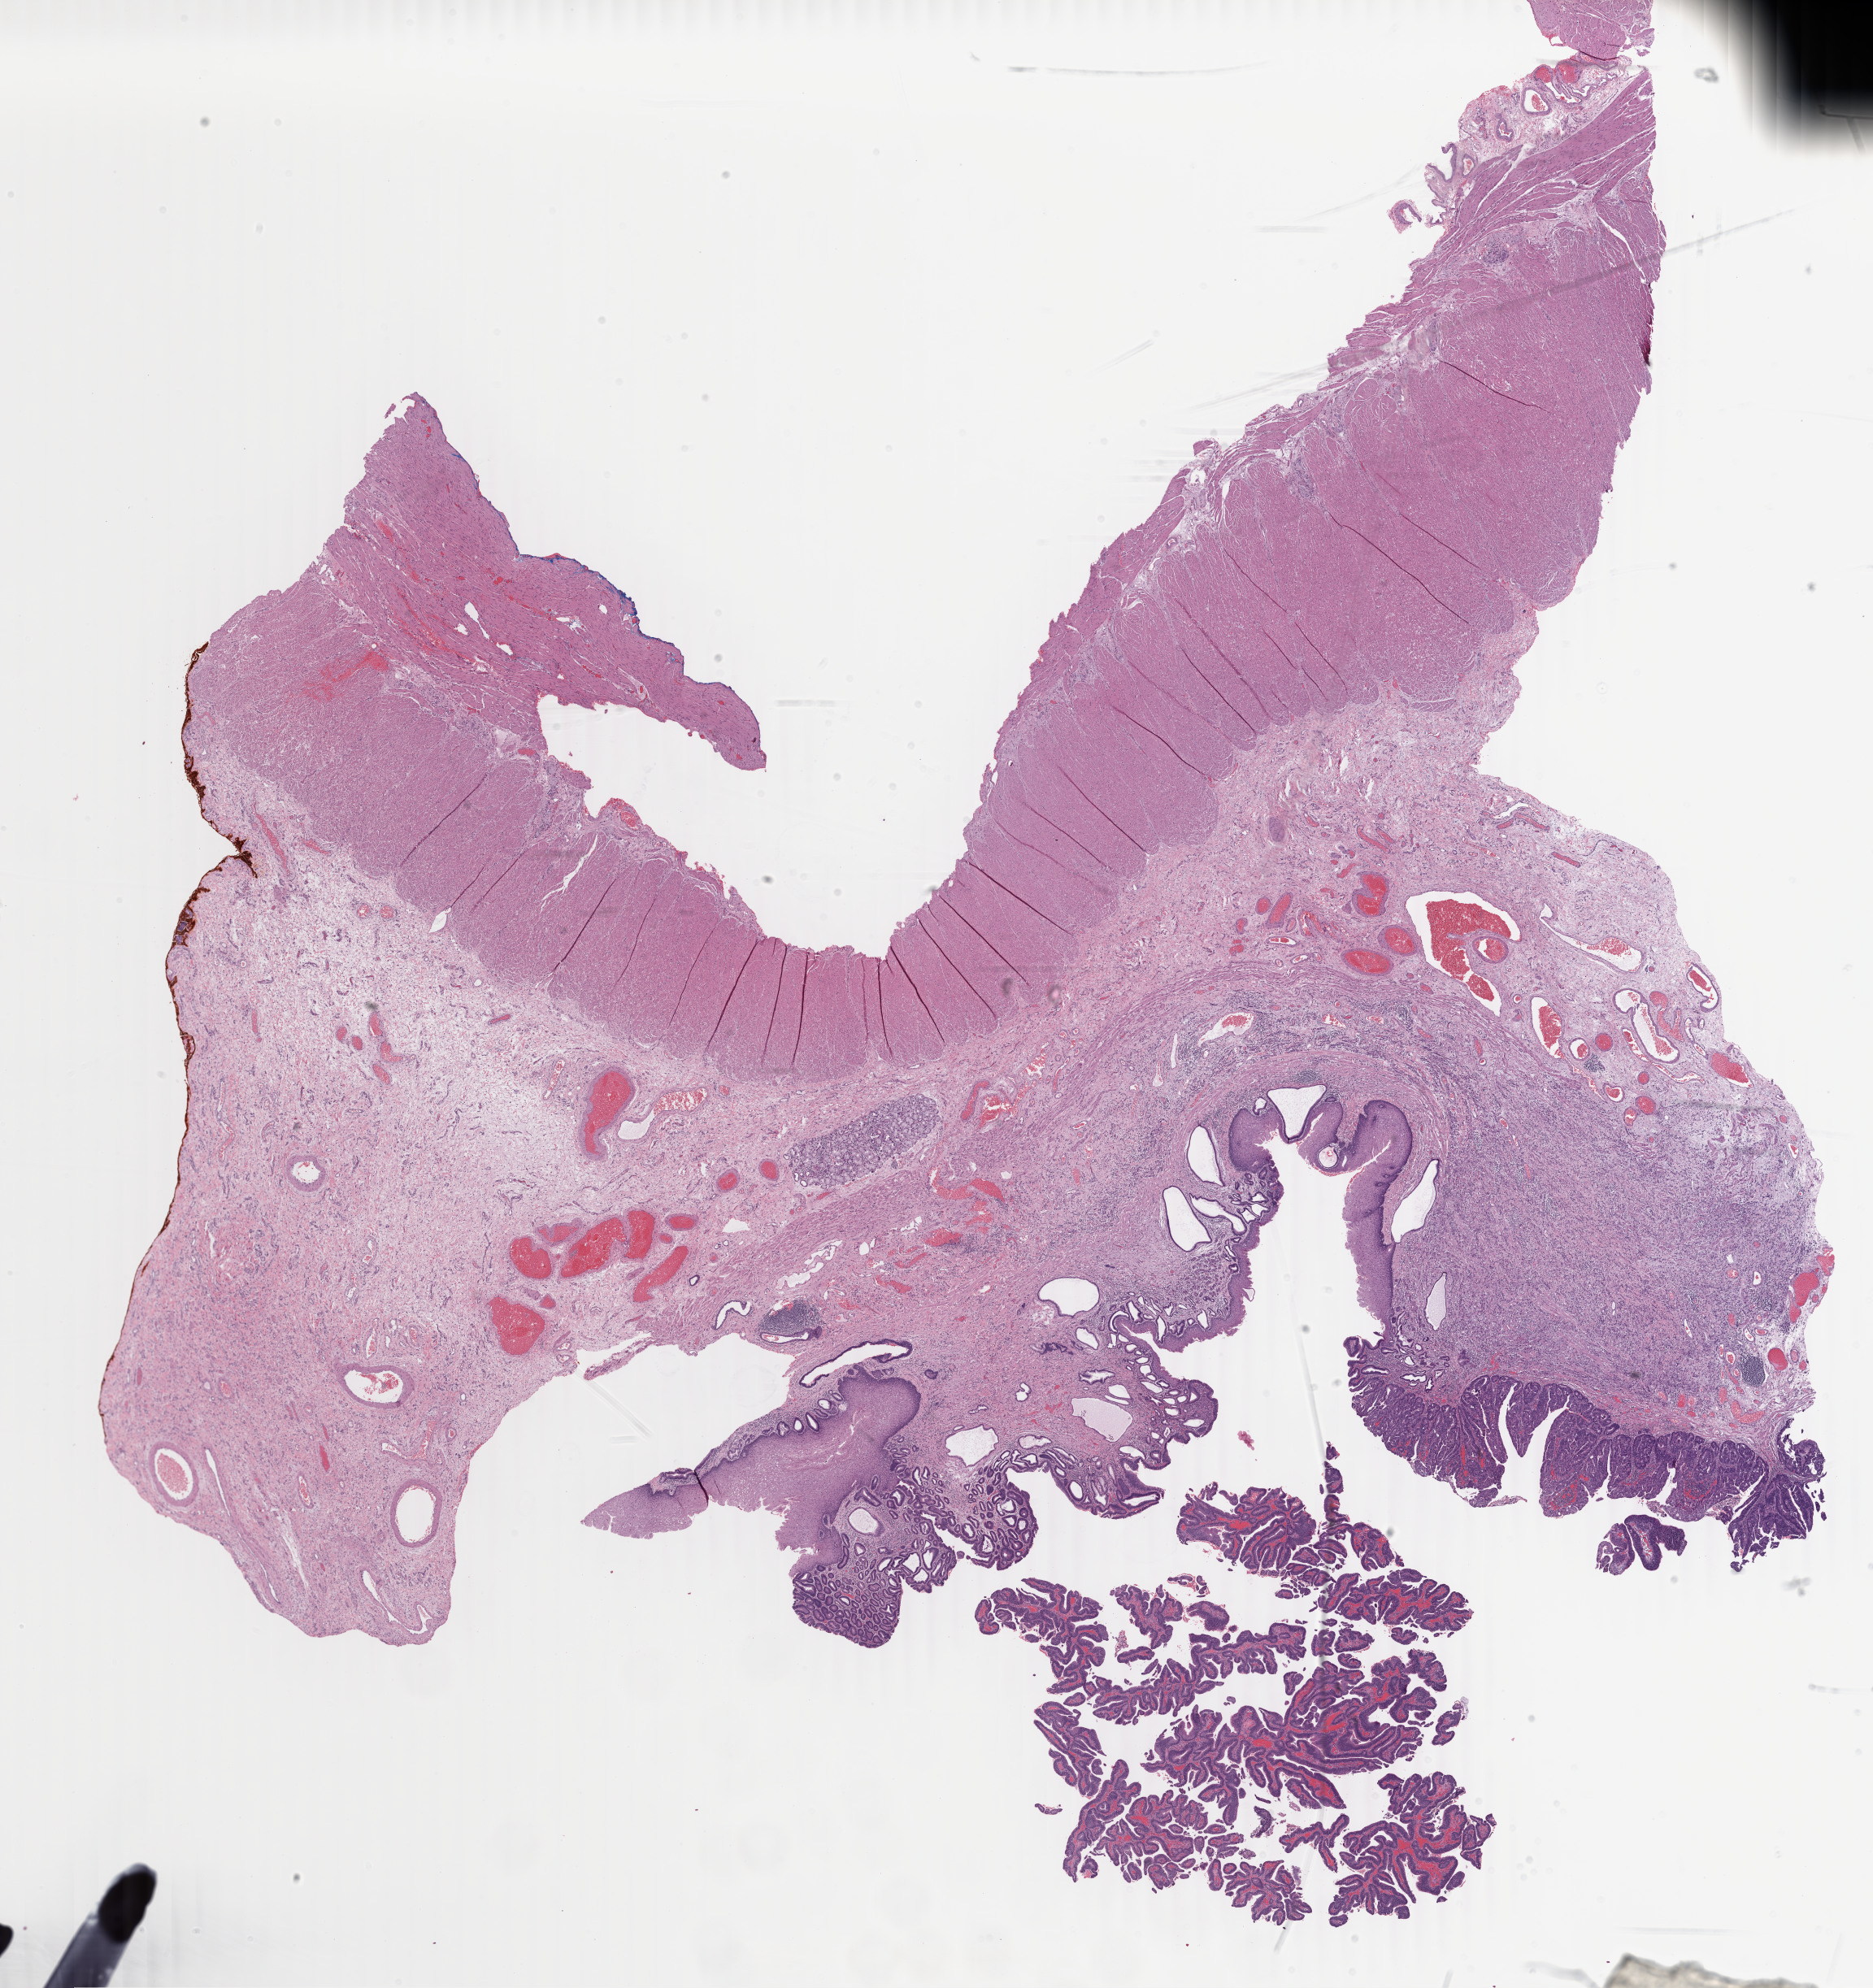
Digitized H&E tissue section (whole slide), shown as a low-resolution overview of the whole scanned area (about 18.3 x 19.5 mm, from a 40x scan), formalin-fixed paraffin-embedded (FFPE) diagnostic section, primary tumour sample from the esophagus. Male patient; age at initial diagnosis 74 years. Histologic grade: GX (grade cannot be assessed).
Histologic diagnosis: Adenocarcinoma, NOS (lower third of esophagus). AJCC pathologic stage: I (7th edition).